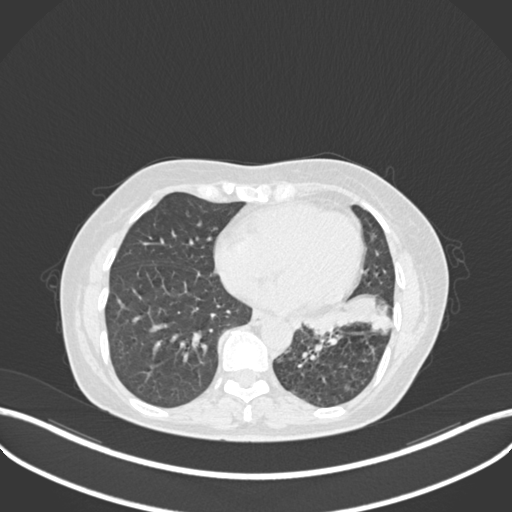
Chest CT, one axial slice. Slice 95 of 270 in the series (ordered by position). 120 kVp. Lung window (W 1500 / L -600 HU). 1 mm slice thickness. 512 × 512 image matrix. Female patient, age 63 years. Case-level facts recorded for this patient, not image findings: clinical TNM (as recorded): T1b N0 M0; histopathological grade: G2-3.
Outlined on this slice (rectangle marked by the reading radiologist):
- lung tumour (recorded histology: adenocarcinoma): box from (x=302, y=293) to (x=394, y=343) px